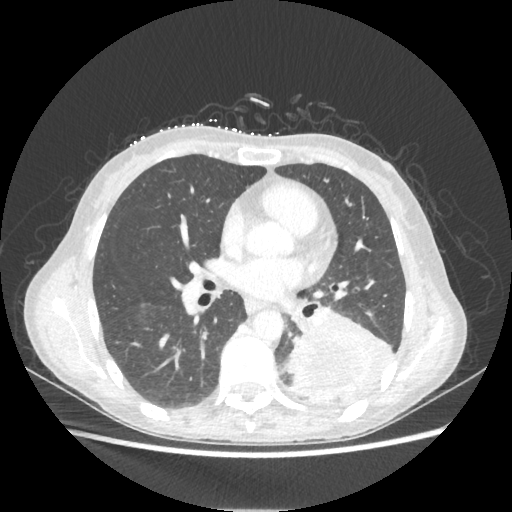
Chest CT, one axial slice; slice 112 of 221 in the series (ordered by position); 80 kVp; lung window (W 1500 / L -600 HU); 1.25 mm slice thickness; 512 × 512 image matrix, field of view 360 × 360 mm. Female patient, age 53 years. From the clinical record (not read from this slice): clinical TNM (as recorded): T3 N0 M0.
Structures marked on this image (bounding box drawn by a radiologist):
- lung tumour (recorded histology: adenocarcinoma): bounding box <285,307,394,400> (left, top, right, bottom; pixels)